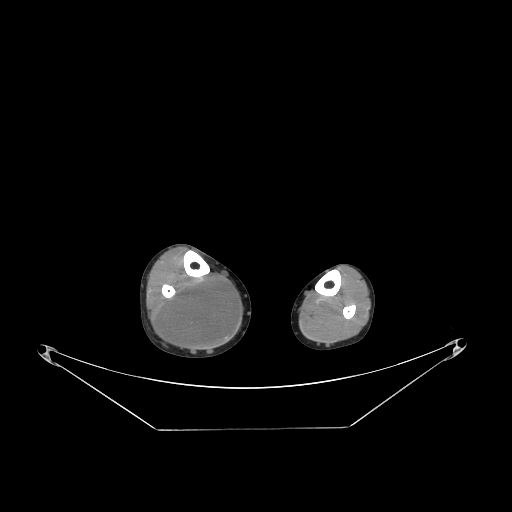
CT of an extremity soft-tissue mass (from a PET/CT study), one axial slice; position 85 of 267 along the scan axis; soft-tissue window (W 400 / L 40 HU); 3.75 mm slice thickness; 512 × 512 image matrix, field of view 500 × 500 mm. Male patient. From the clinical record (not read from this slice): histological type: liposarcoma - round cell; grade: high; site of the primary tumour: right calf.
Annotated regions visible in this slice (expert contour drawn on MRI and transferred to this co-registered scan by the dataset authors):
- gross tumour volume (mass): bounding box (x1, y1, x2, y2) in pixels: (162, 276, 239, 346)